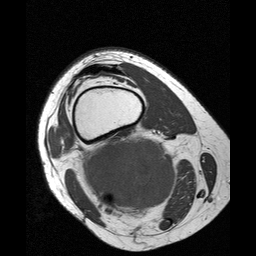
MRI of an extremity soft-tissue mass, one axial slice; position 21 of 25 along the scan axis; 256 × 256 image matrix. Female patient. Case-level facts recorded for this patient, not image findings: histological type: liposarcoma; site of the primary tumour: right thigh.
Annotated regions visible in this slice (outlined manually by an expert reader):
- gross tumour volume (mass): bounding box [x1, y1, x2, y2] px = [75, 132, 177, 220]